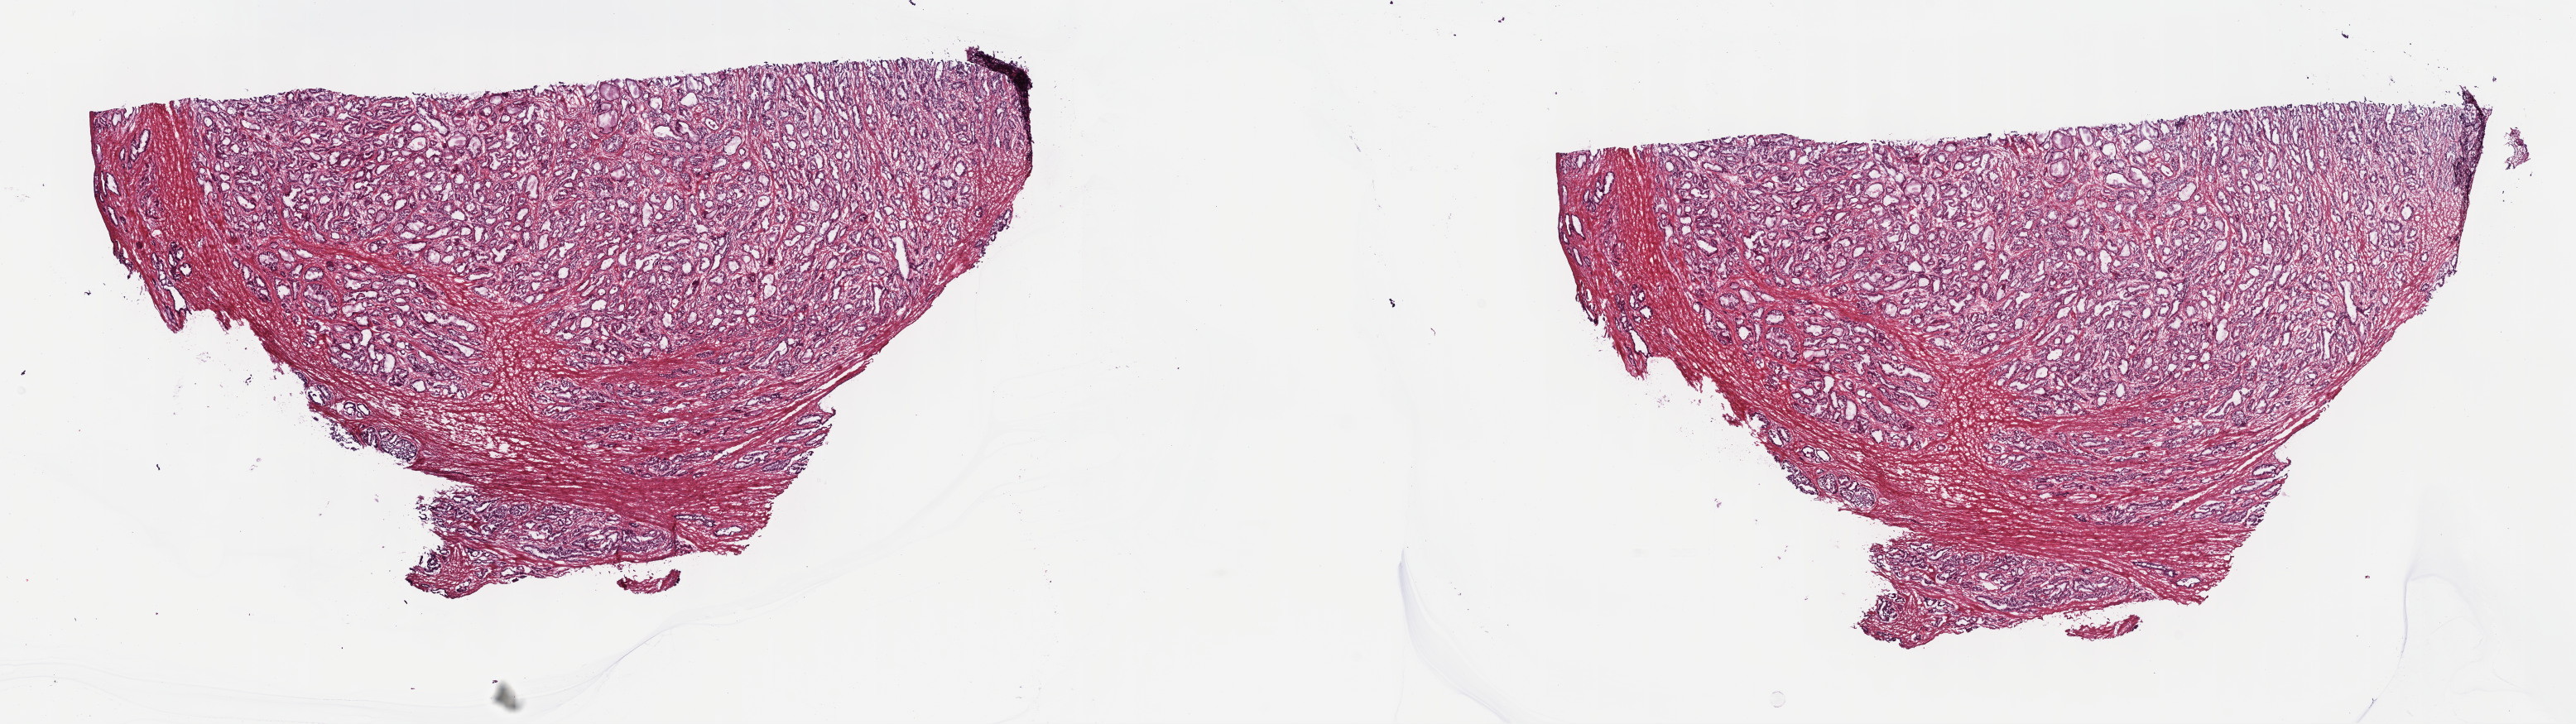
Hematoxylin and eosin (H&E) stained whole-slide image, low-resolution overview of the scanned area, about 25.2 x 7.1 mm (slide scanned at 40x), frozen section from the top of the tissue portion, sample: primary tumour, prostate. Male, age 68 years at initial diagnosis. Gleason score: 6 (3+3). Slide review estimates, as recorded: tumour cells 70%, tumour nuclei 90%, normal cells 0%, stromal cells 30%, necrosis 0%. Infiltration values recorded for this section: lymphocyte infiltration 0%, monocyte infiltration 0%, neutrophil infiltration 0%.
Pathologic diagnosis: Adenocarcinoma, NOS. Lymph nodes positive (case pathology): 0 of 12 examined. Laterality: bilateral.